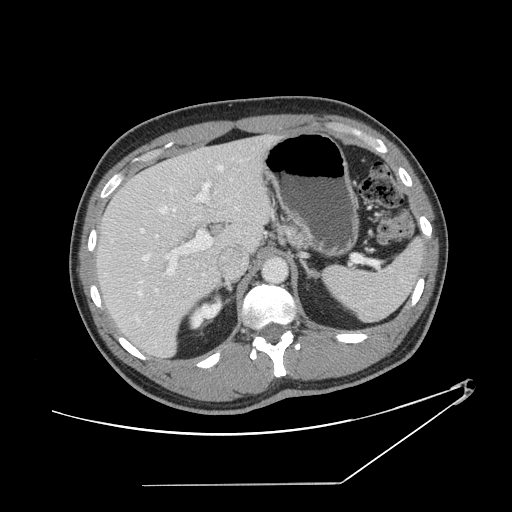
Contrast-enhanced abdominal CT, one axial slice. Position 92 of 152 along the scan axis. 120 kVp. Soft-tissue window (W 400 / L 40 HU). 512 × 512 image matrix, field of view 432 × 432 mm. Male patient, age 45 years. Case-level facts recorded for this patient, not image findings: diagnosis: colorectal cancer liver metastases, imaged before liver resection; multiple liver metastases: no; largest metastasis: 1 cm; disease in both lobes: no.
Annotated regions visible in this slice (expert manual segmentation):
- hepatic veins: bounding box (x1, y1, x2, y2) in pixels: (111, 164, 239, 296)
- liver: (98, 137, 270, 356)
- planned liver remnant (the part of the liver to remain after resection): (98, 155, 227, 356)
- portal vein (with intrahepatic branches): (140, 182, 212, 314)